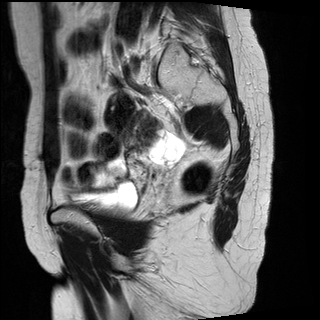
Pelvic MRI for cervical cancer, one sagittal slice. Slice 9 of 29 in the series (ordered by position). T2-weighted. 1.5 T. TE 89 ms, TR 2930 ms. 4 mm slice thickness. 320 × 320 image matrix, field of view 260 × 260 mm. Female patient, age 45 years.
Annotated regions visible in this slice (manually delineated by an expert):
- uterus and cervix: bounding box <123,109,156,150> (left, top, right, bottom; pixels)